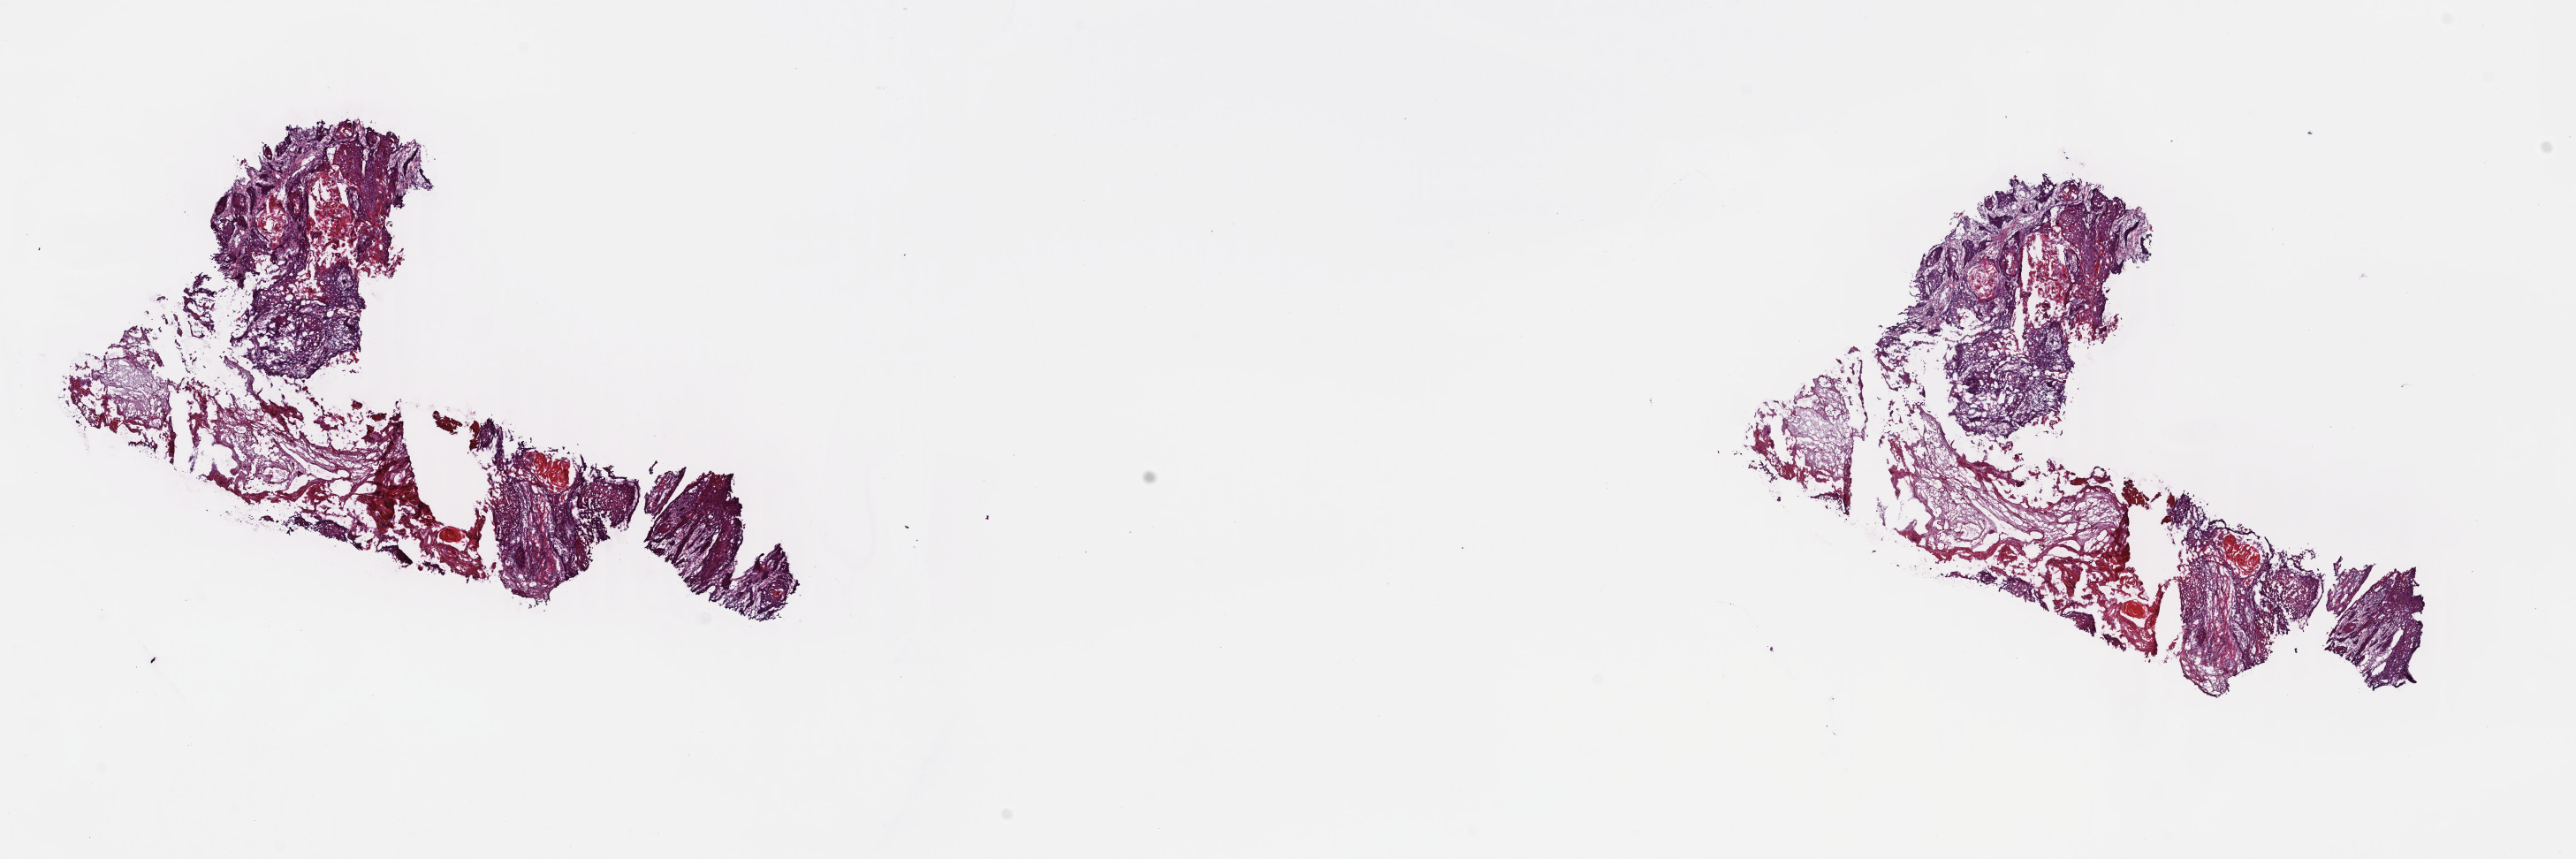
Hematoxylin and eosin (H&E) stained whole-slide image, whole scanned area (about 22.9 x 7.6 mm) shown as a low-resolution overview; frozen section; primary tumour sample from the head and neck. Male patient; age at initial diagnosis 47 years. Histologic grade: G2 (moderately differentiated). Pathologist review of this section (percent, as recorded): tumour cells 60%, tumour nuclei 60%, normal cells 0%, stromal cells 40%, necrosis 0%. Infiltration values recorded for this section: lymphocyte infiltration 100%, monocyte infiltration 0%, neutrophil infiltration 0%.
AJCC pathologic stage: IVA (5th edition). Diagnosis: Squamous cell carcinoma, NOS.